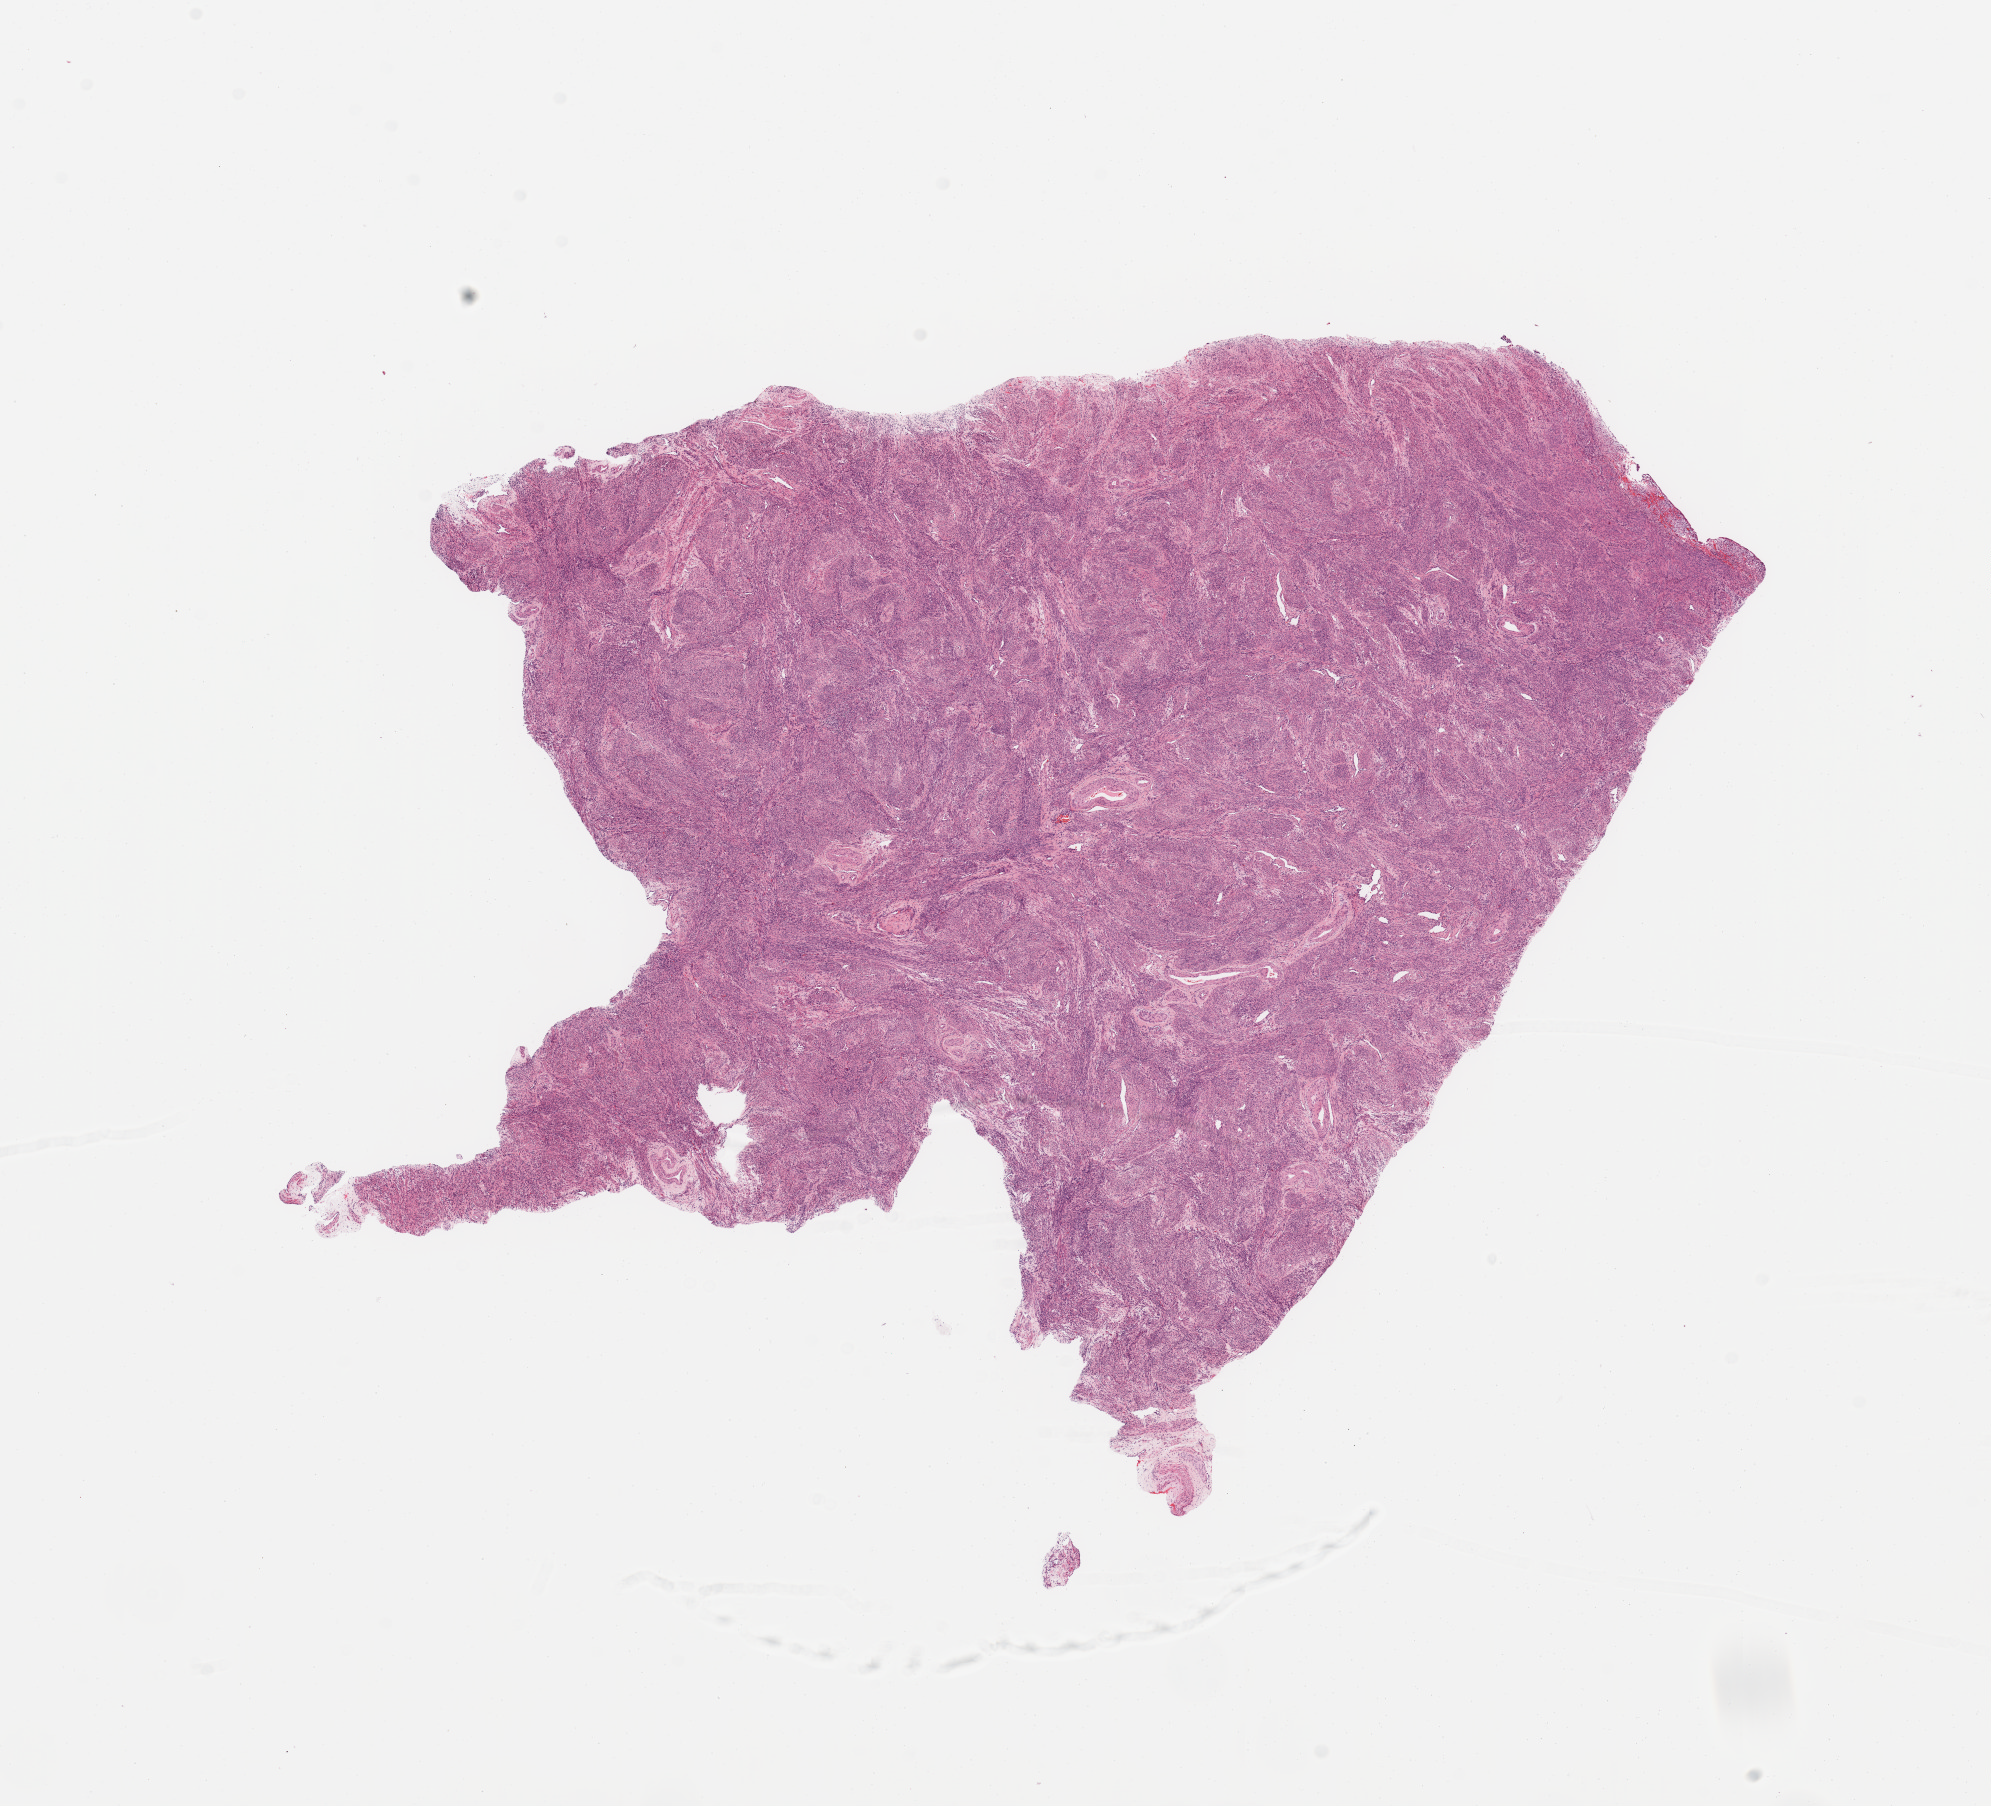
H&E whole-slide image, a low-resolution overview of the entire scanned area, about 15.8 x 14.3 mm. Normal (non-tumour) tissue sample, uterus. Patient: female, age 55 years.
- this section: normal (non-tumour) tissue from the same patient
- patient diagnosis: Endometrioid adenocarcinoma, NOS